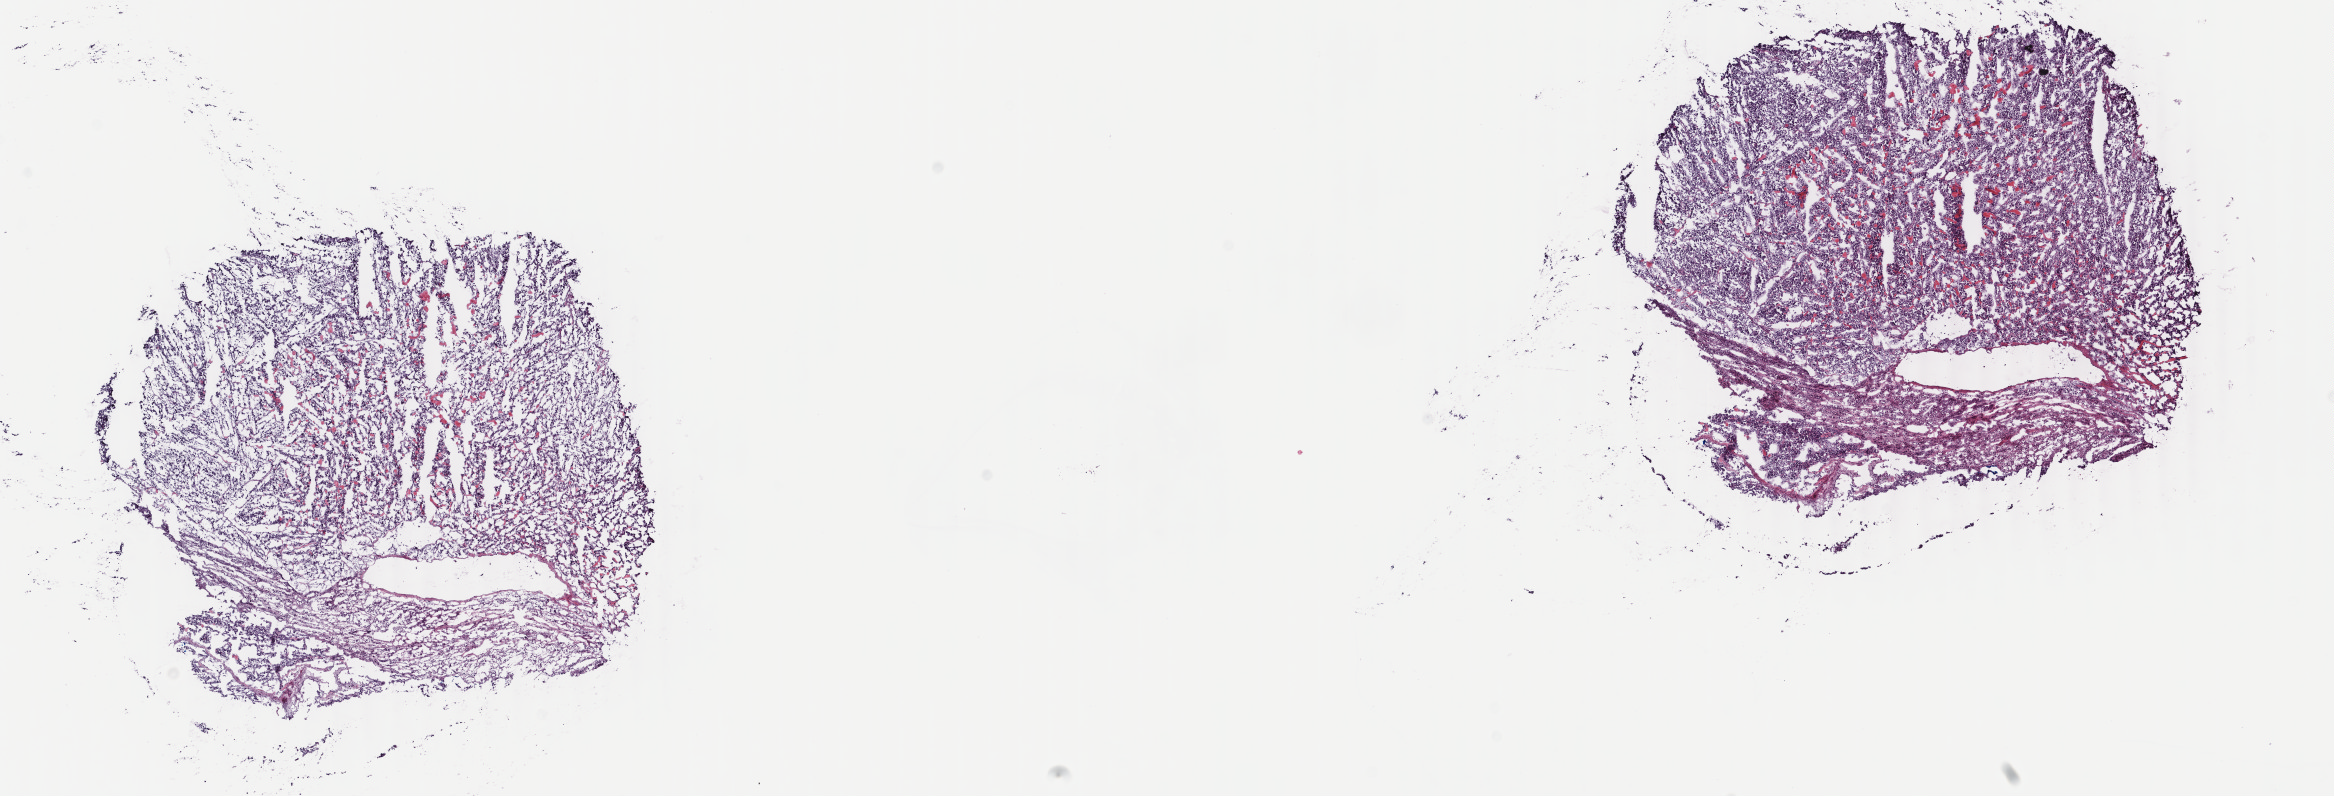
Whole-slide histology image, Hematoxylin and eosin (H&E) stained — shown as a low-resolution overview of the whole scanned area (about 18.6 x 6.3 mm, slide scanned at 40x). Frozen section from the top of the tissue portion. Sample: primary tumour, adrenal gland. Male patient; age at initial diagnosis 49 years. Composition of this section per pathologist review: tumour cells 90%, tumour nuclei 100%, normal cells 0%, stromal cells 10%, necrosis 0%. Infiltration values recorded for this section: lymphocyte infiltration 0%, monocyte infiltration 0%, neutrophil infiltration 0%.
Pathologic diagnosis: Papillary adenocarcinoma, NOS (thyroid gland).